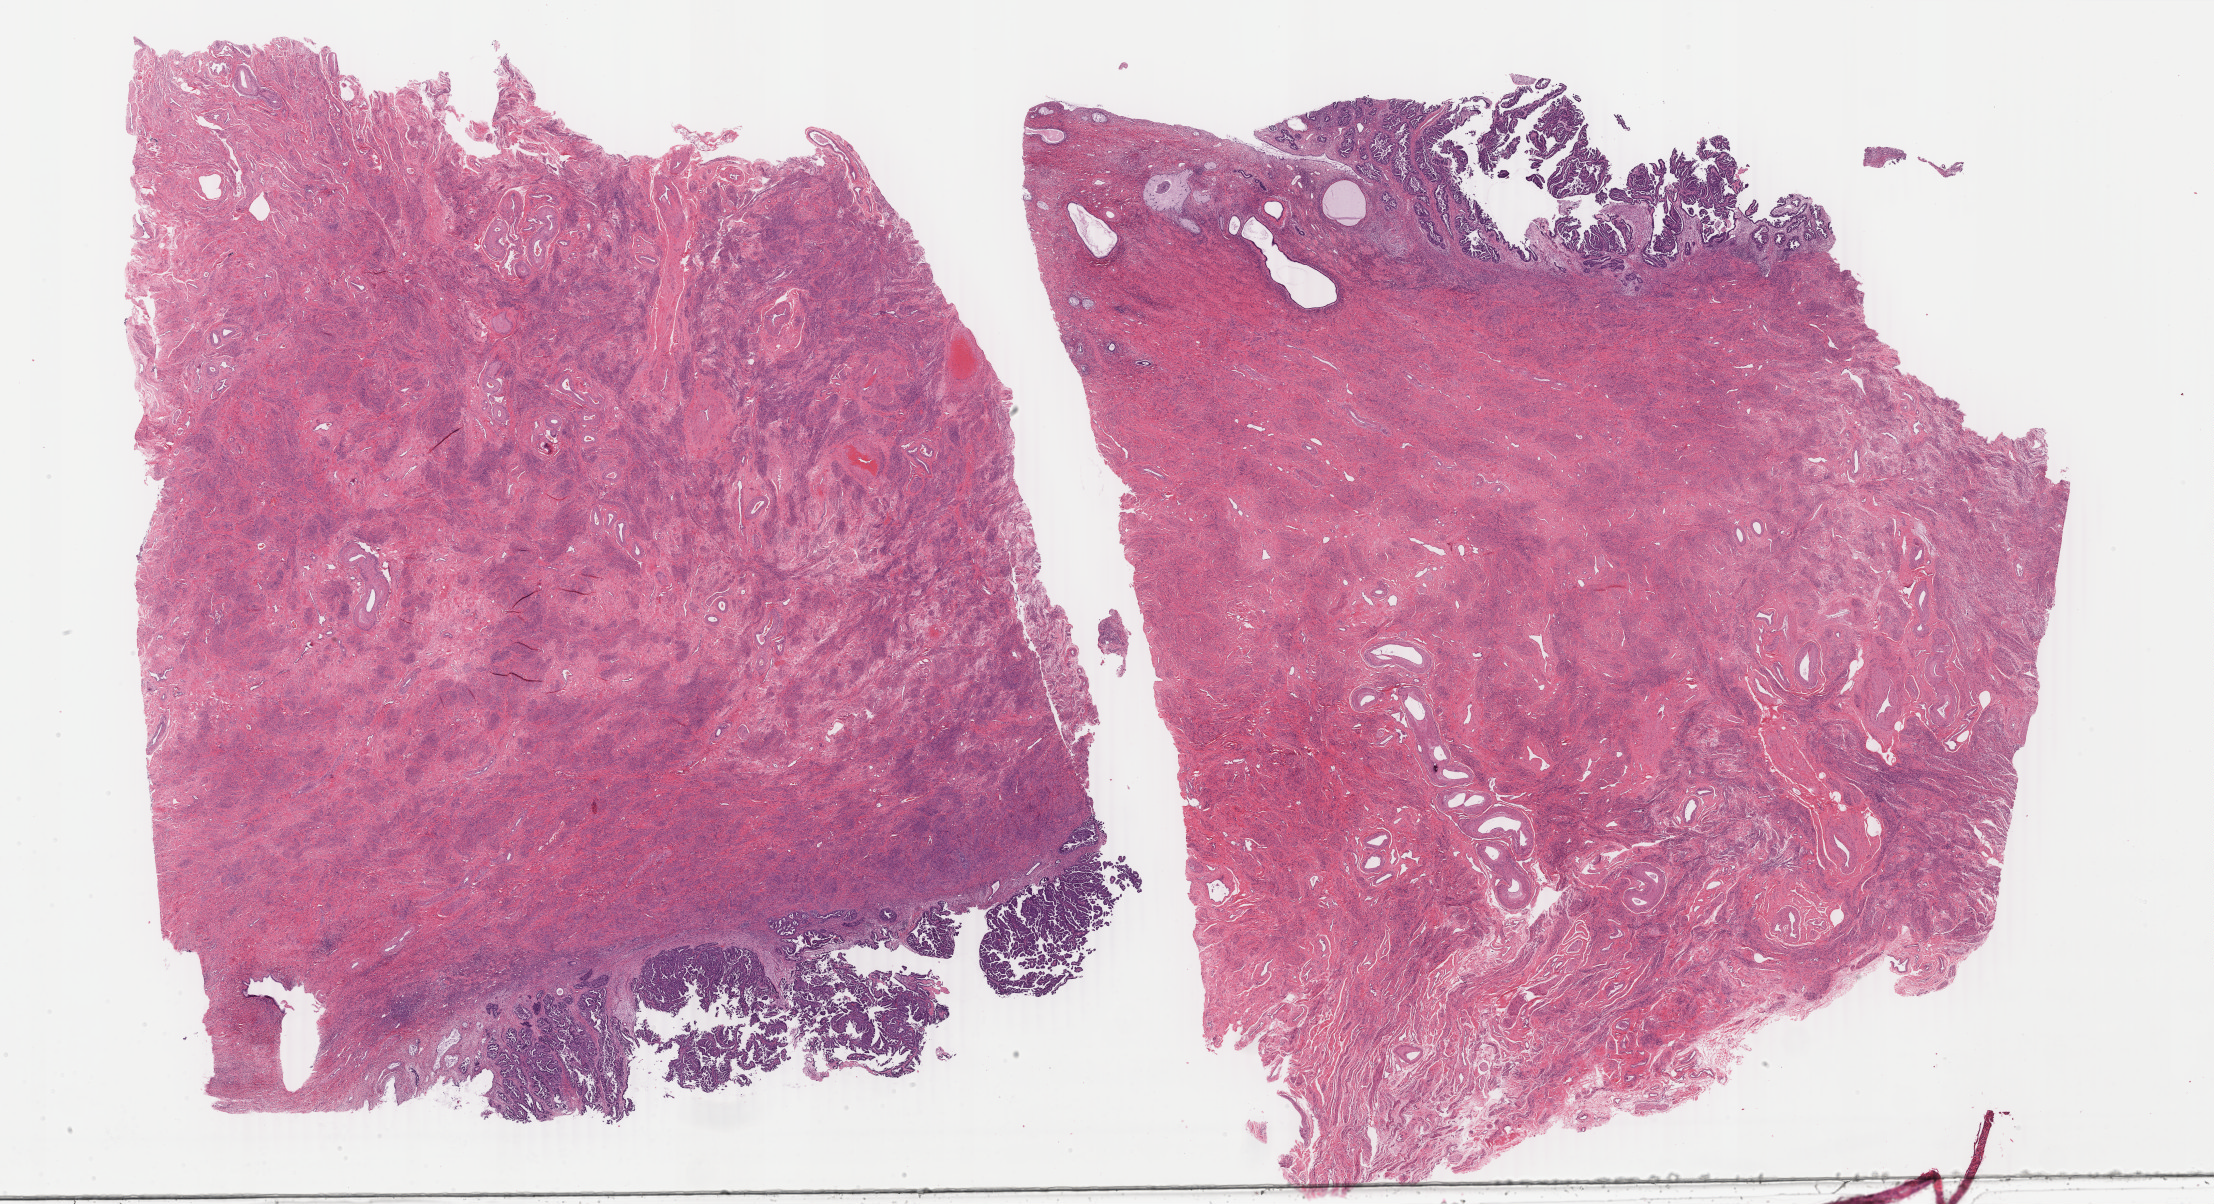
H&E-stained whole-slide image — low-resolution overview of the scanned area, about 35.2 x 19.2 mm (from a 40x scan), FFPE section, sample: primary tumour, uterus. Female patient; age at initial diagnosis 70 years. Histologic grade: high grade.
Histologic diagnosis: Serous cystadenocarcinoma, NOS (endometrium). FIGO stage: IIIC.